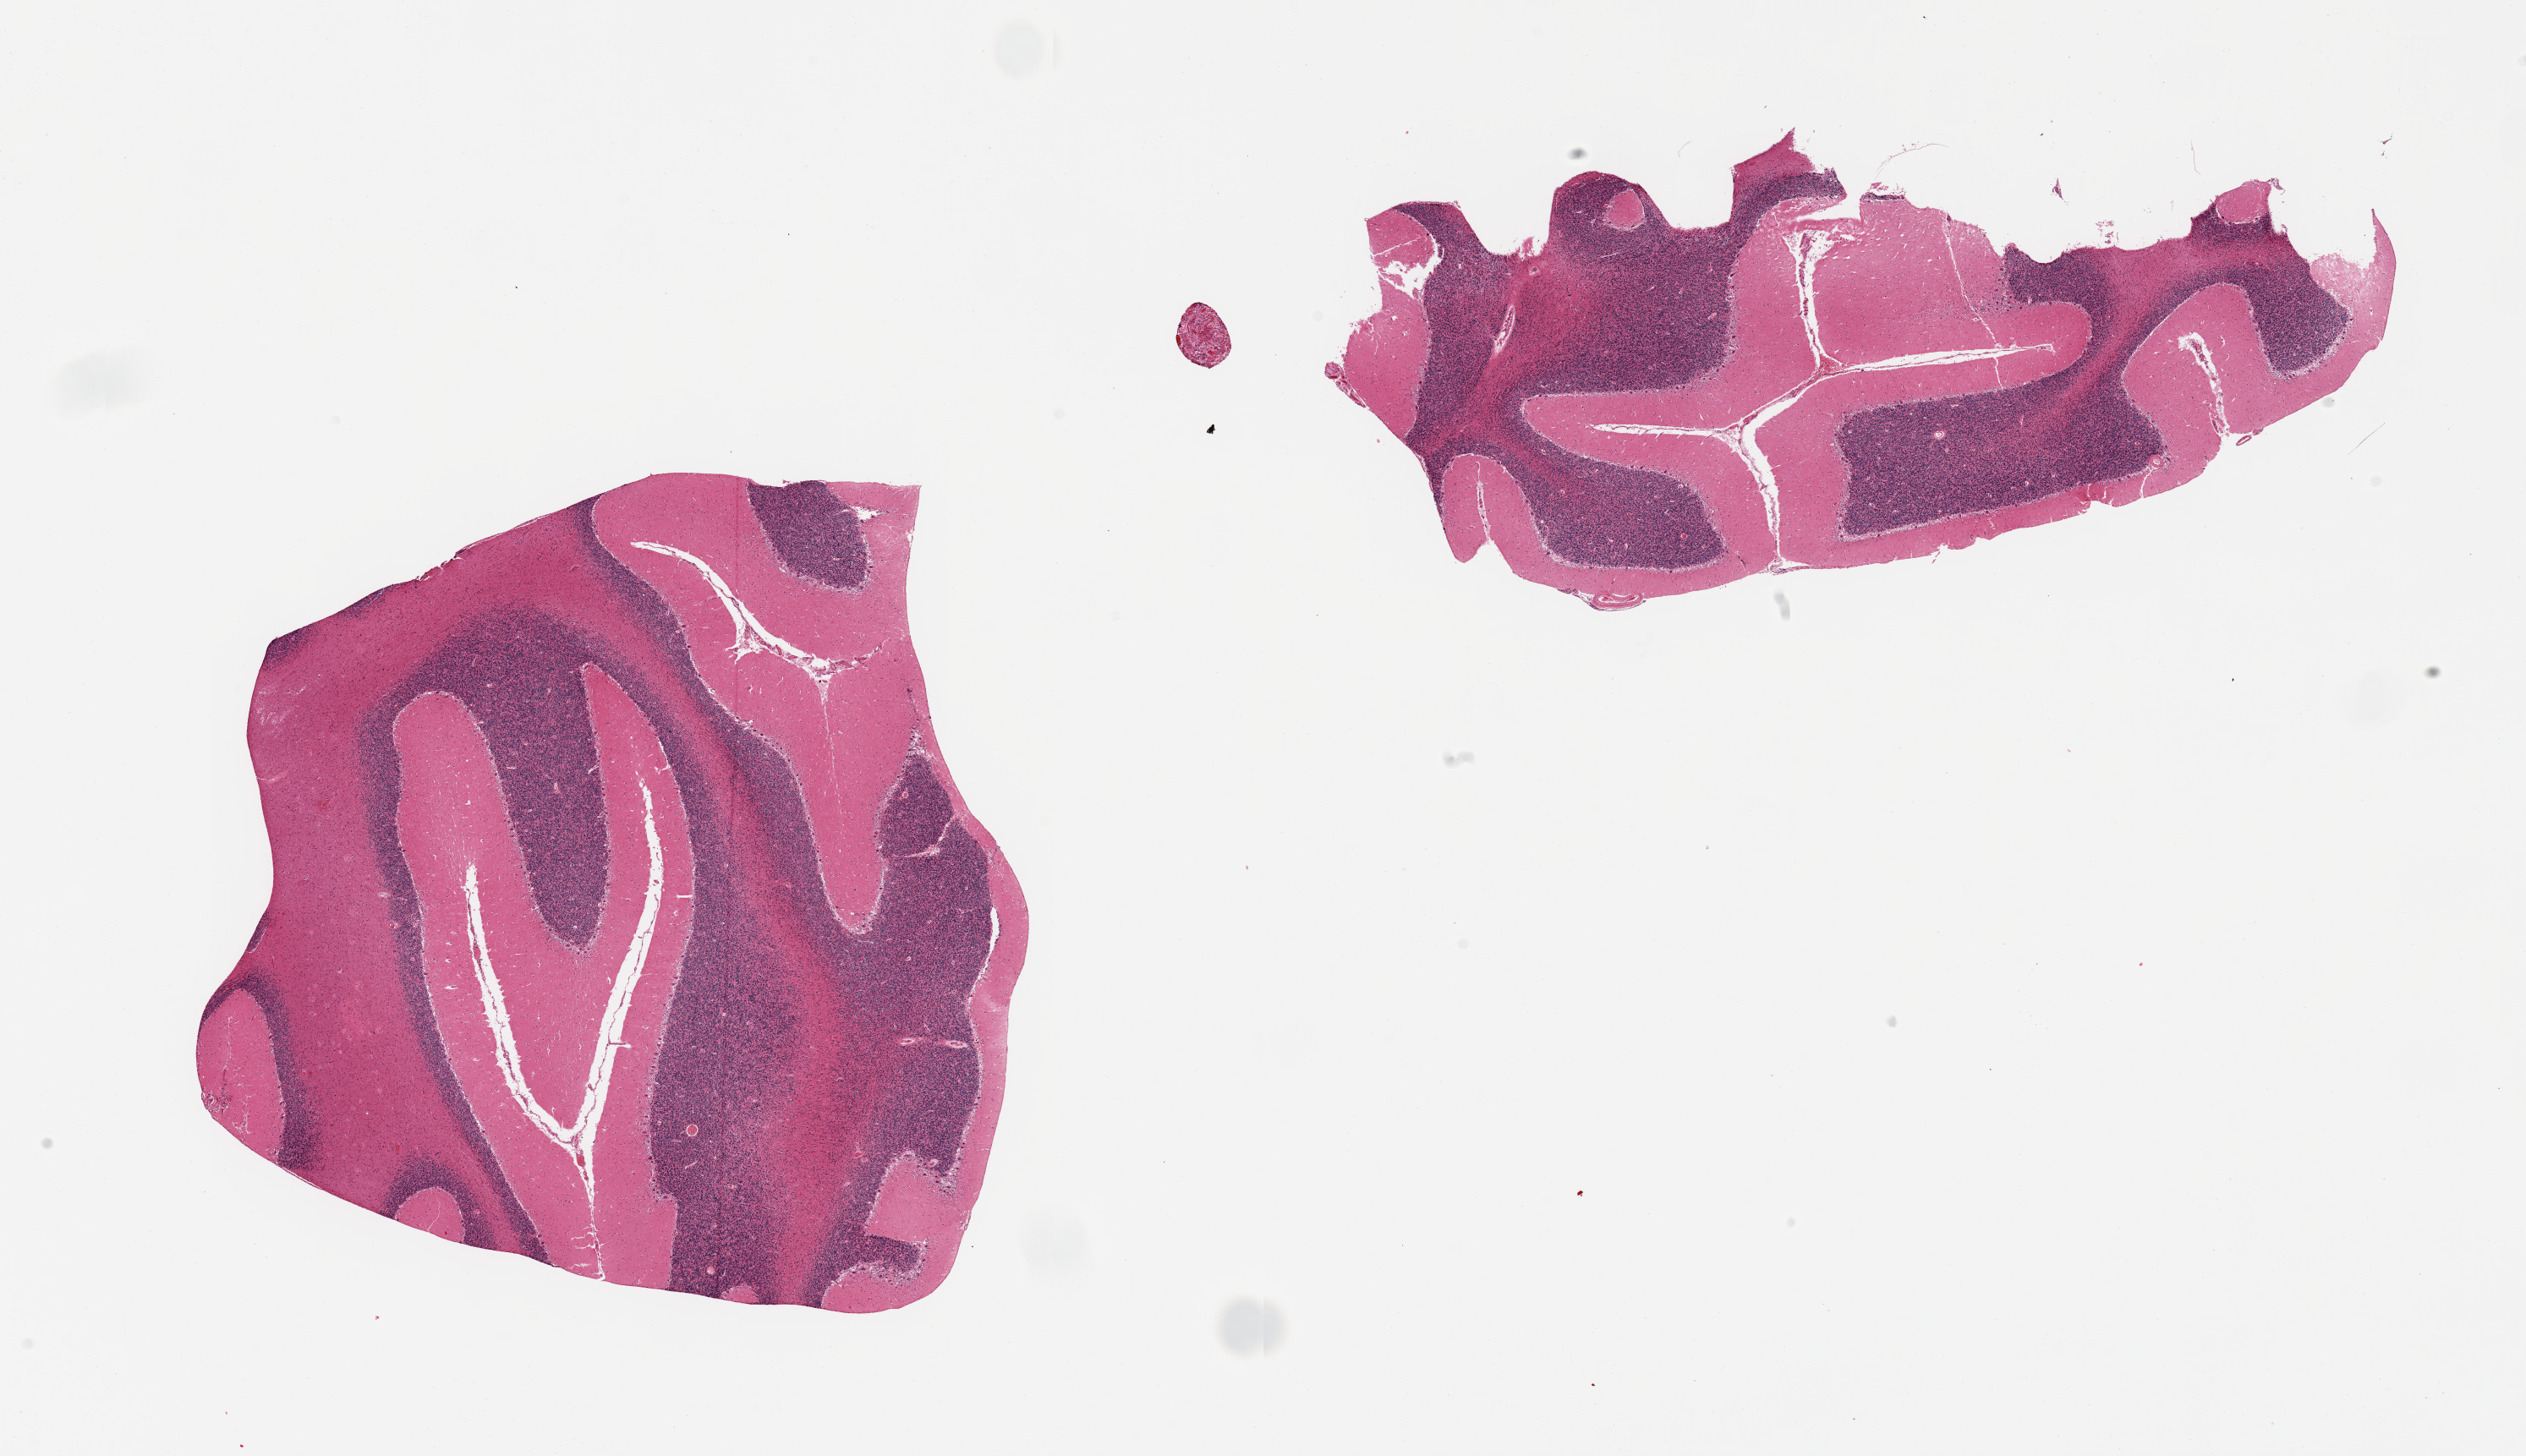
Haematoxylin and eosin whole-slide image — low-resolution overview of the scanned area, about 23.6 x 13.6 mm, PAXgene-fixed, paraffin-embedded tissue, sampled site (target tissue): cerebellum, tissue donor sample.
Reviewer comment on this tissue sample: 2 pieces.